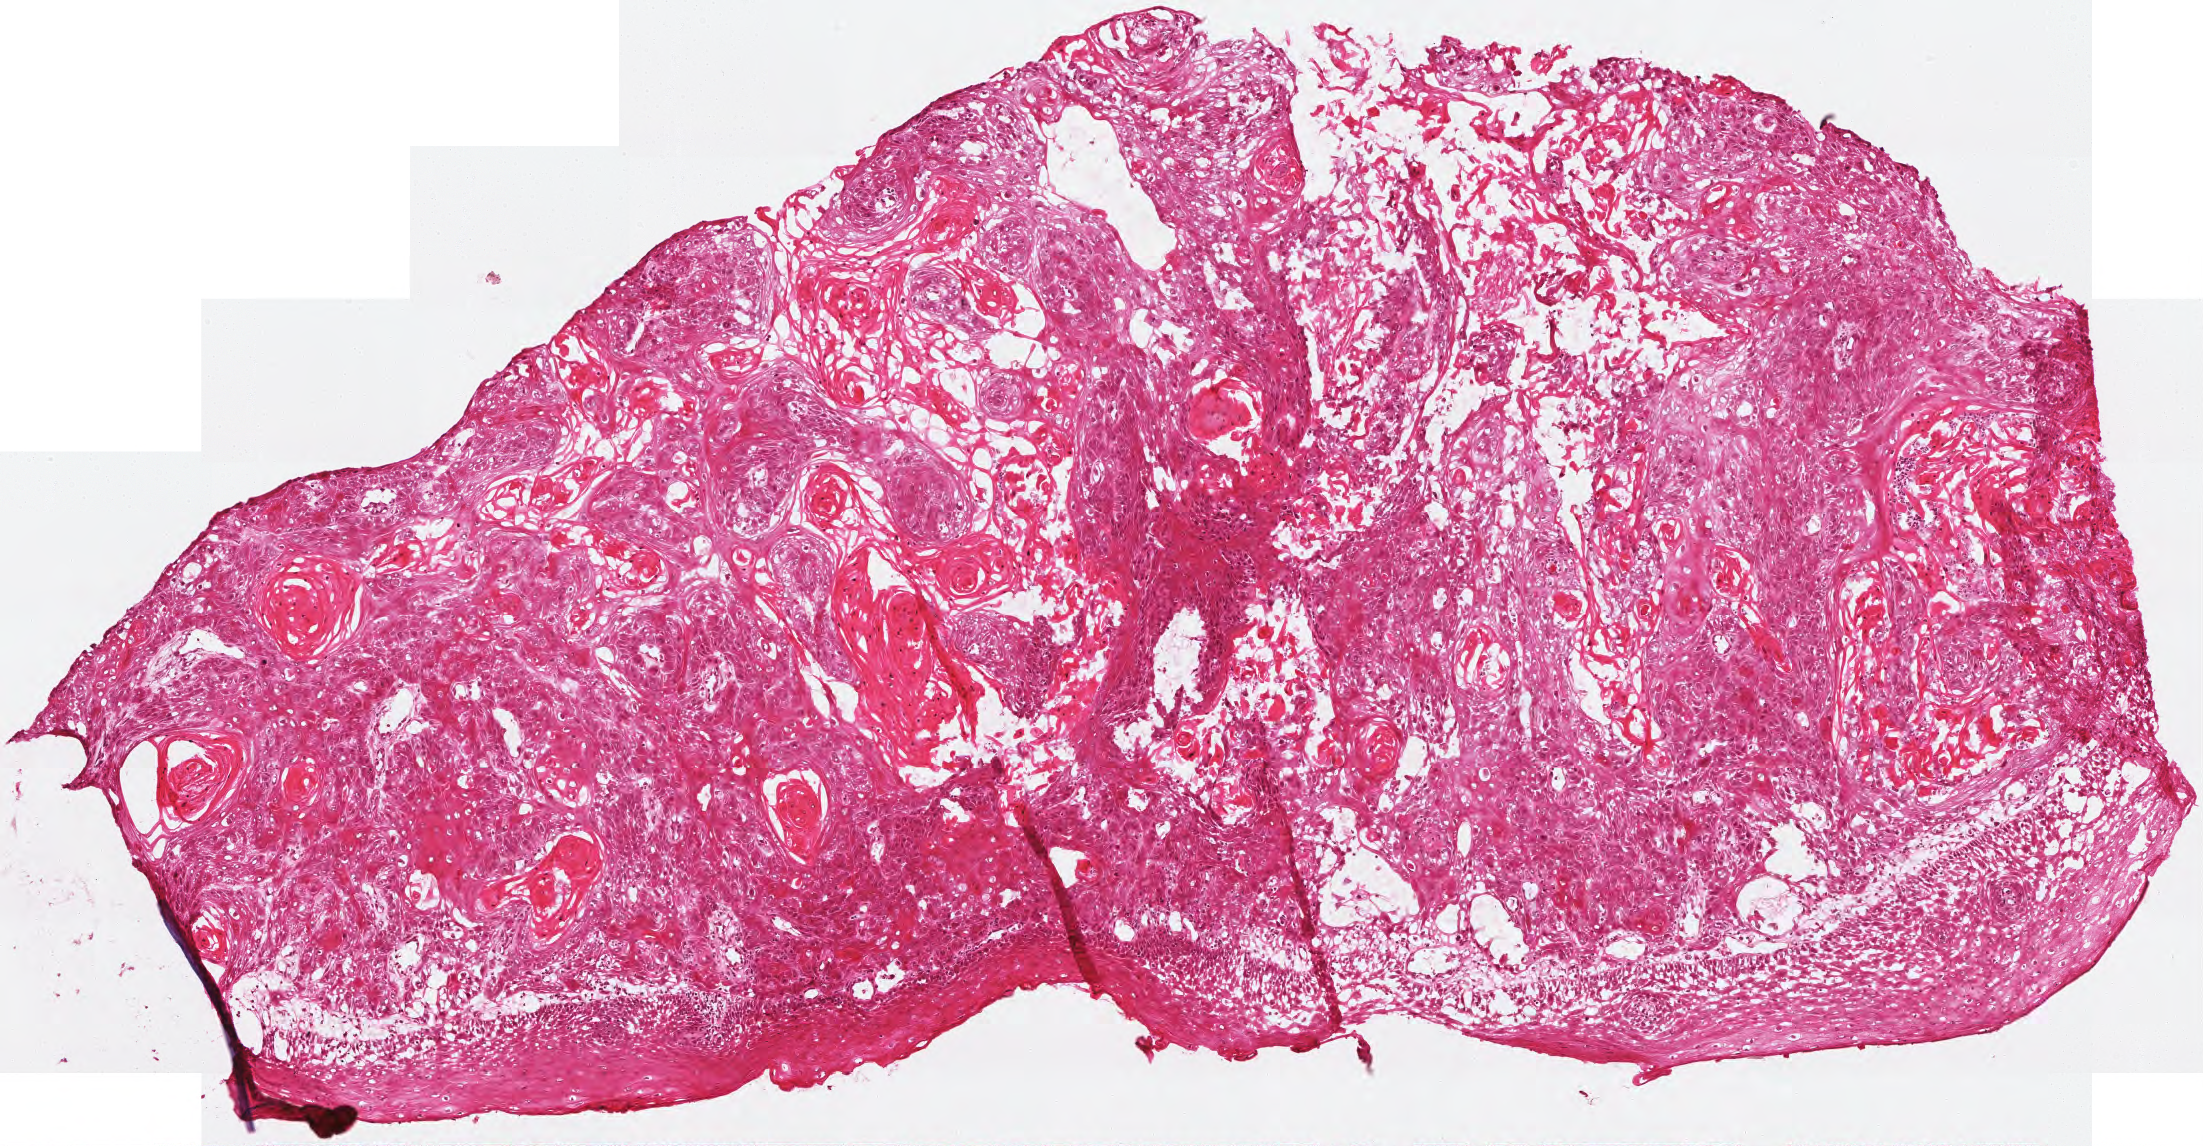
H&E-stained whole-slide image, low-resolution overview of the scanned area, about 4.4 x 2.3 mm, frozen section, primary tumour sample from the head and neck. Female patient; age at initial diagnosis 68 years. Histologic grade: G2 (moderately differentiated). Slide review estimates, as recorded: tumour cells 85%, tumour nuclei 85%, normal cells 5%, stromal cells 10%, necrosis 0%.
Diagnosis: Squamous cell carcinoma, NOS. AJCC pathologic stage: II (7th edition). TNM: T2 N0.